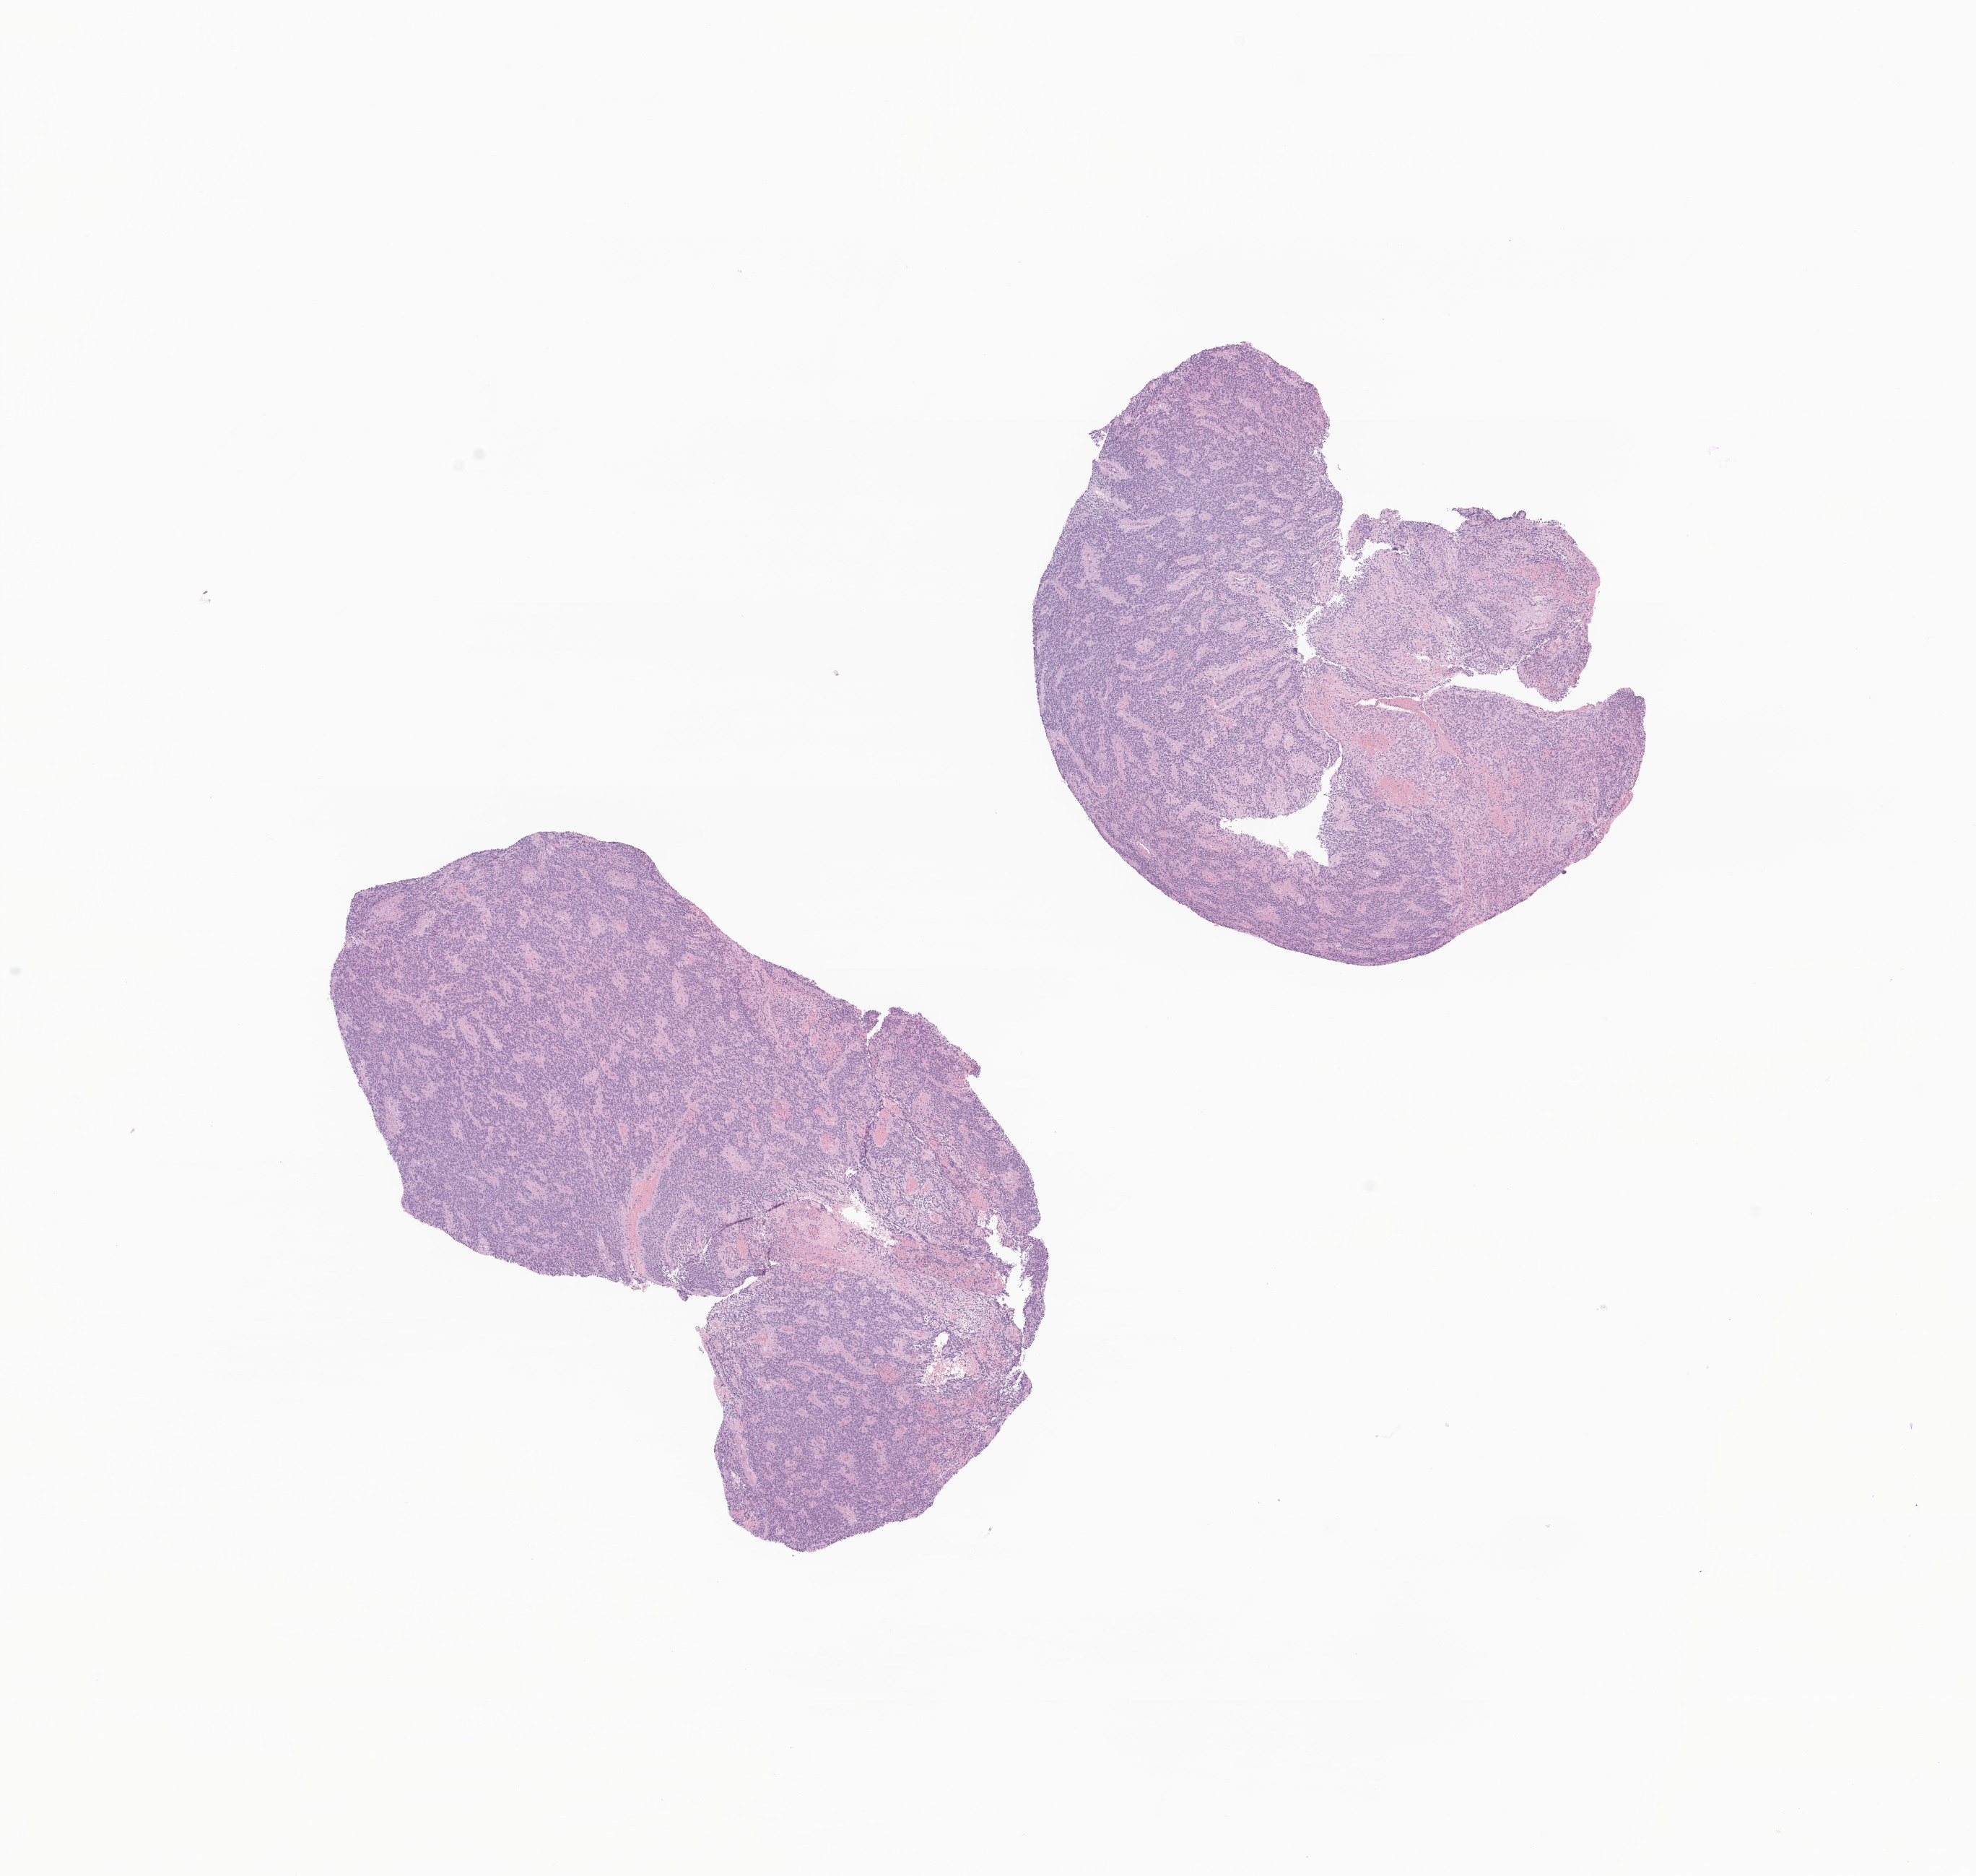
Hematoxylin and eosin (H&E) whole-slide image of tumor tissue from the brain stem — whole scanned area (about 11.5 x 11.0 mm) shown as a low-resolution overview; formalin-fixed paraffin-embedded section. Female patient, age 373 days.
Recorded diagnosis: Ependymoma, anaplastic.